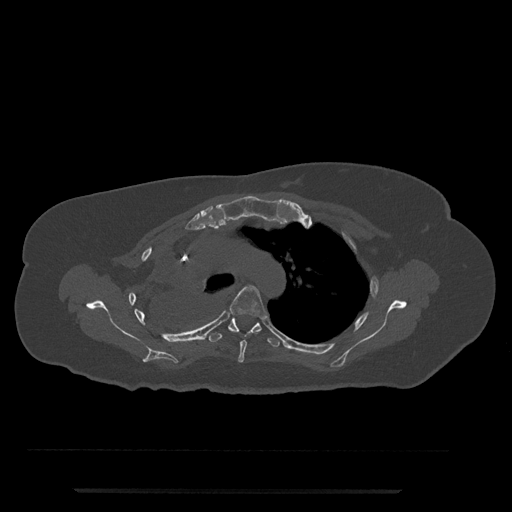
CT including the spine, one axial slice; reconstruction kernel Br40s/3; 120 kVp; bone window (W 1800 / L 400 HU); 512 × 512 image matrix. Patient: female, 51 years. From the clinical record (not read from this slice): primary cancer: neuro.
Outlined on this slice (semi-automatic segmentation, software-assisted and operator-edited):
- T4 vertebra: box from (x=196, y=285) to (x=267, y=363) px
- T5 vertebra: (x=209, y=318)–(x=281, y=347)